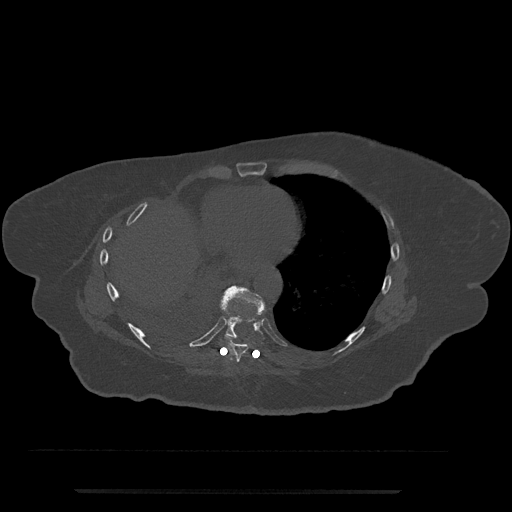
CT including the spine, one axial slice. Position 368 of 797 along the scan axis. Reconstruction kernel Br40s/3. Bone window (W 1800 / L 400 HU). 0.5 mm slice thickness. 512 × 512 image matrix. Patient: female, 51 years. Case-level facts recorded for this patient, not image findings: primary cancer: neuro.
Outlined on this slice (semi-automatically segmented with operator editing):
- T8 vertebra: box from (x=219, y=334) to (x=249, y=362) px
- T9 vertebra: (x=218, y=285)–(x=266, y=339)